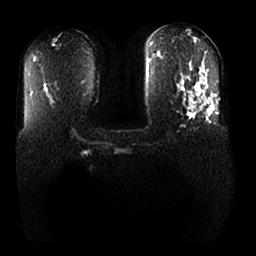
Breast MRI, one axial slice. Diffusion-weighted series; image 2 of 4 stored at this slice position (different b-values; order by instance number). 1.5 T. 4 mm slice thickness. 256 × 256 image matrix, field of view 370 × 370 mm. Female patient.
Structures marked on this image (expert manual segmentation):
- tumour on diffusion-weighted imaging: bounding box (x1, y1, x2, y2) in pixels: (192, 100, 214, 113)